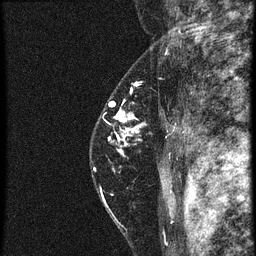
Breast MRI (dynamic contrast-enhanced), one sagittal slice. Position 45 of 60 along the scan axis. 4 images stored at this slice position (order not interpretable as contrast timing). 1.5 T. TE 4.2 ms, TR 20.4 ms. 1.5 mm slice thickness. 256 × 256 image matrix, field of view 180 × 180 mm. Patient: female, 46 years. Case-level facts recorded for this patient, not image findings: setting: breast cancer imaged before/during neoadjuvant chemotherapy; receptor status: triple-negative.
Structures marked on this image (semi-automatically segmented with operator editing):
- analysis volume of interest (the breast-tissue region the enhancement analysis was run in; not a lesion): box from (x=90, y=82) to (x=181, y=185) px
- tumour enhancement mask (voxels above the 90 % enhancement threshold inside the analysis volume of interest): (x=96, y=110)–(x=143, y=171)